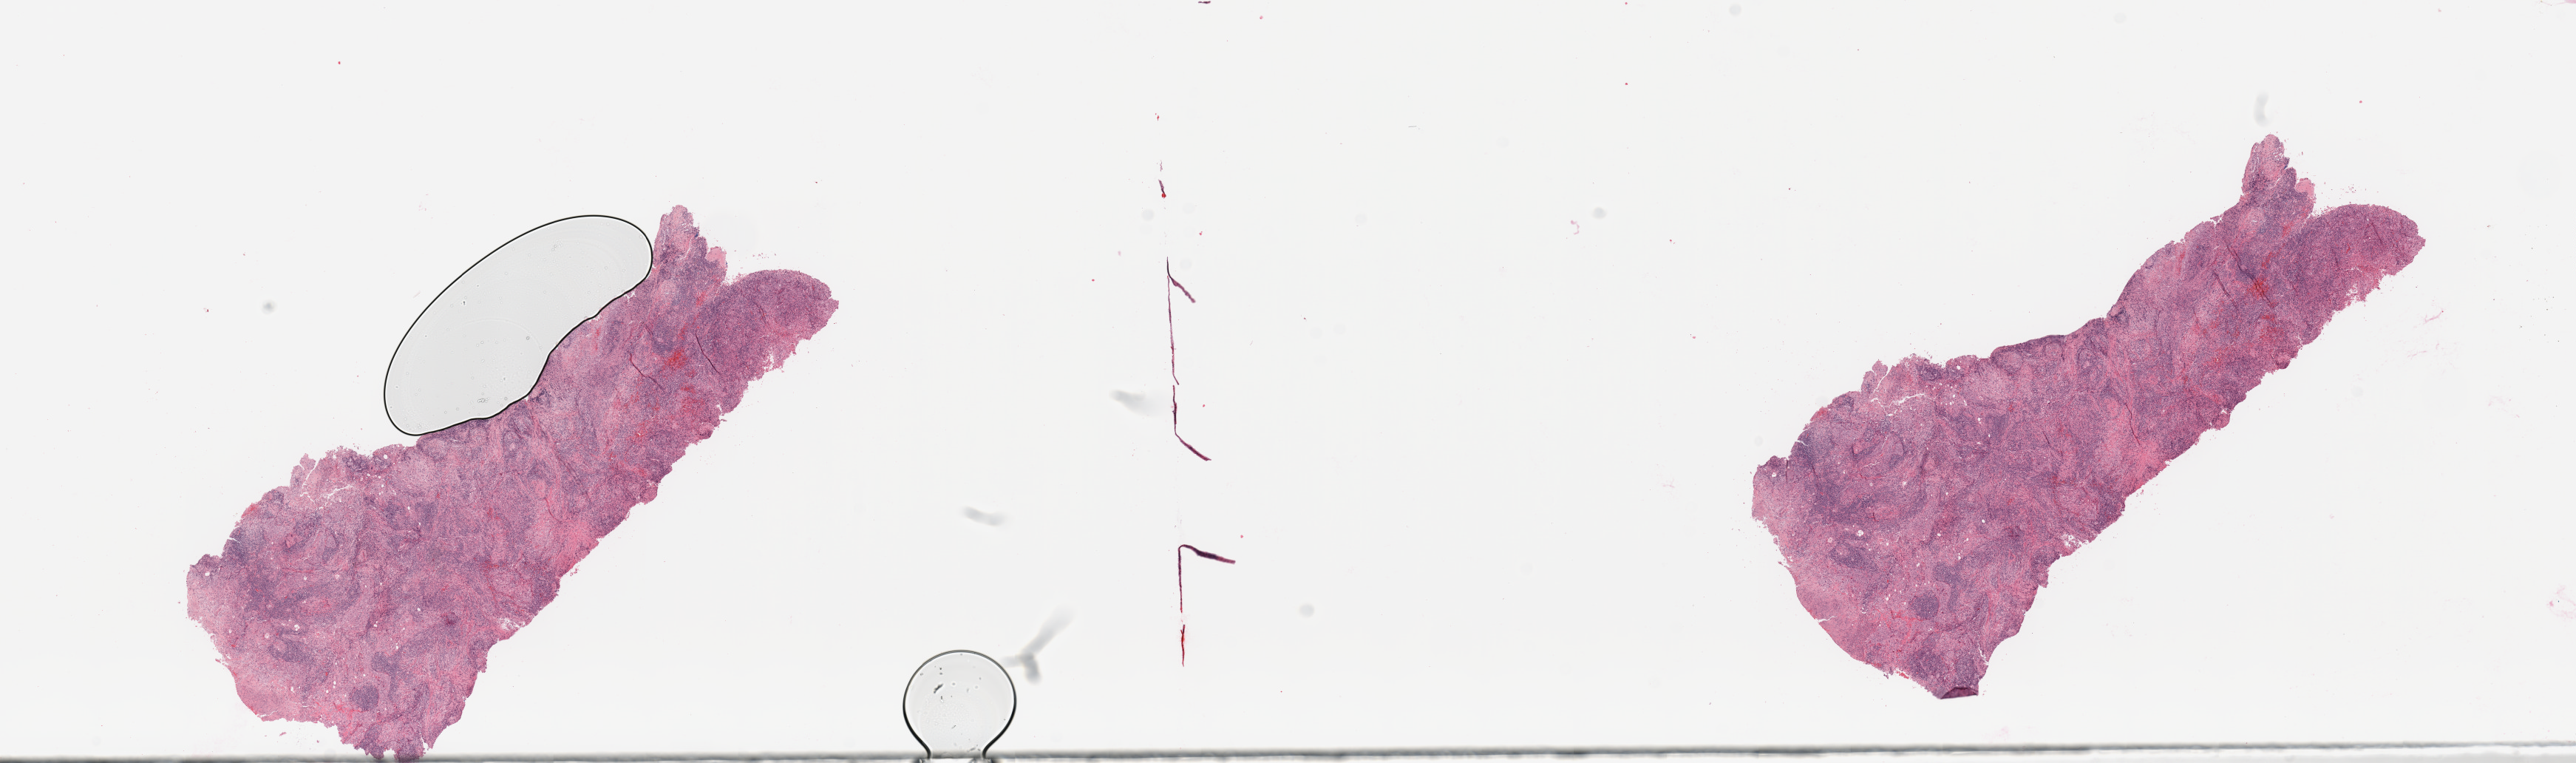
H&E-stained whole-slide image — shown as a low-resolution overview of the whole scanned area (about 27.6 x 8.2 mm, acquisition: 20x scan). Lung, tumour tissue. Patient: female, age 77 years. Histologic grade: G3 (poorly differentiated).
Primary tumour site (as recorded): right lower lobe. Diagnosis: Squamous cell carcinoma, NOS. AJCC pathologic stage: IIA.